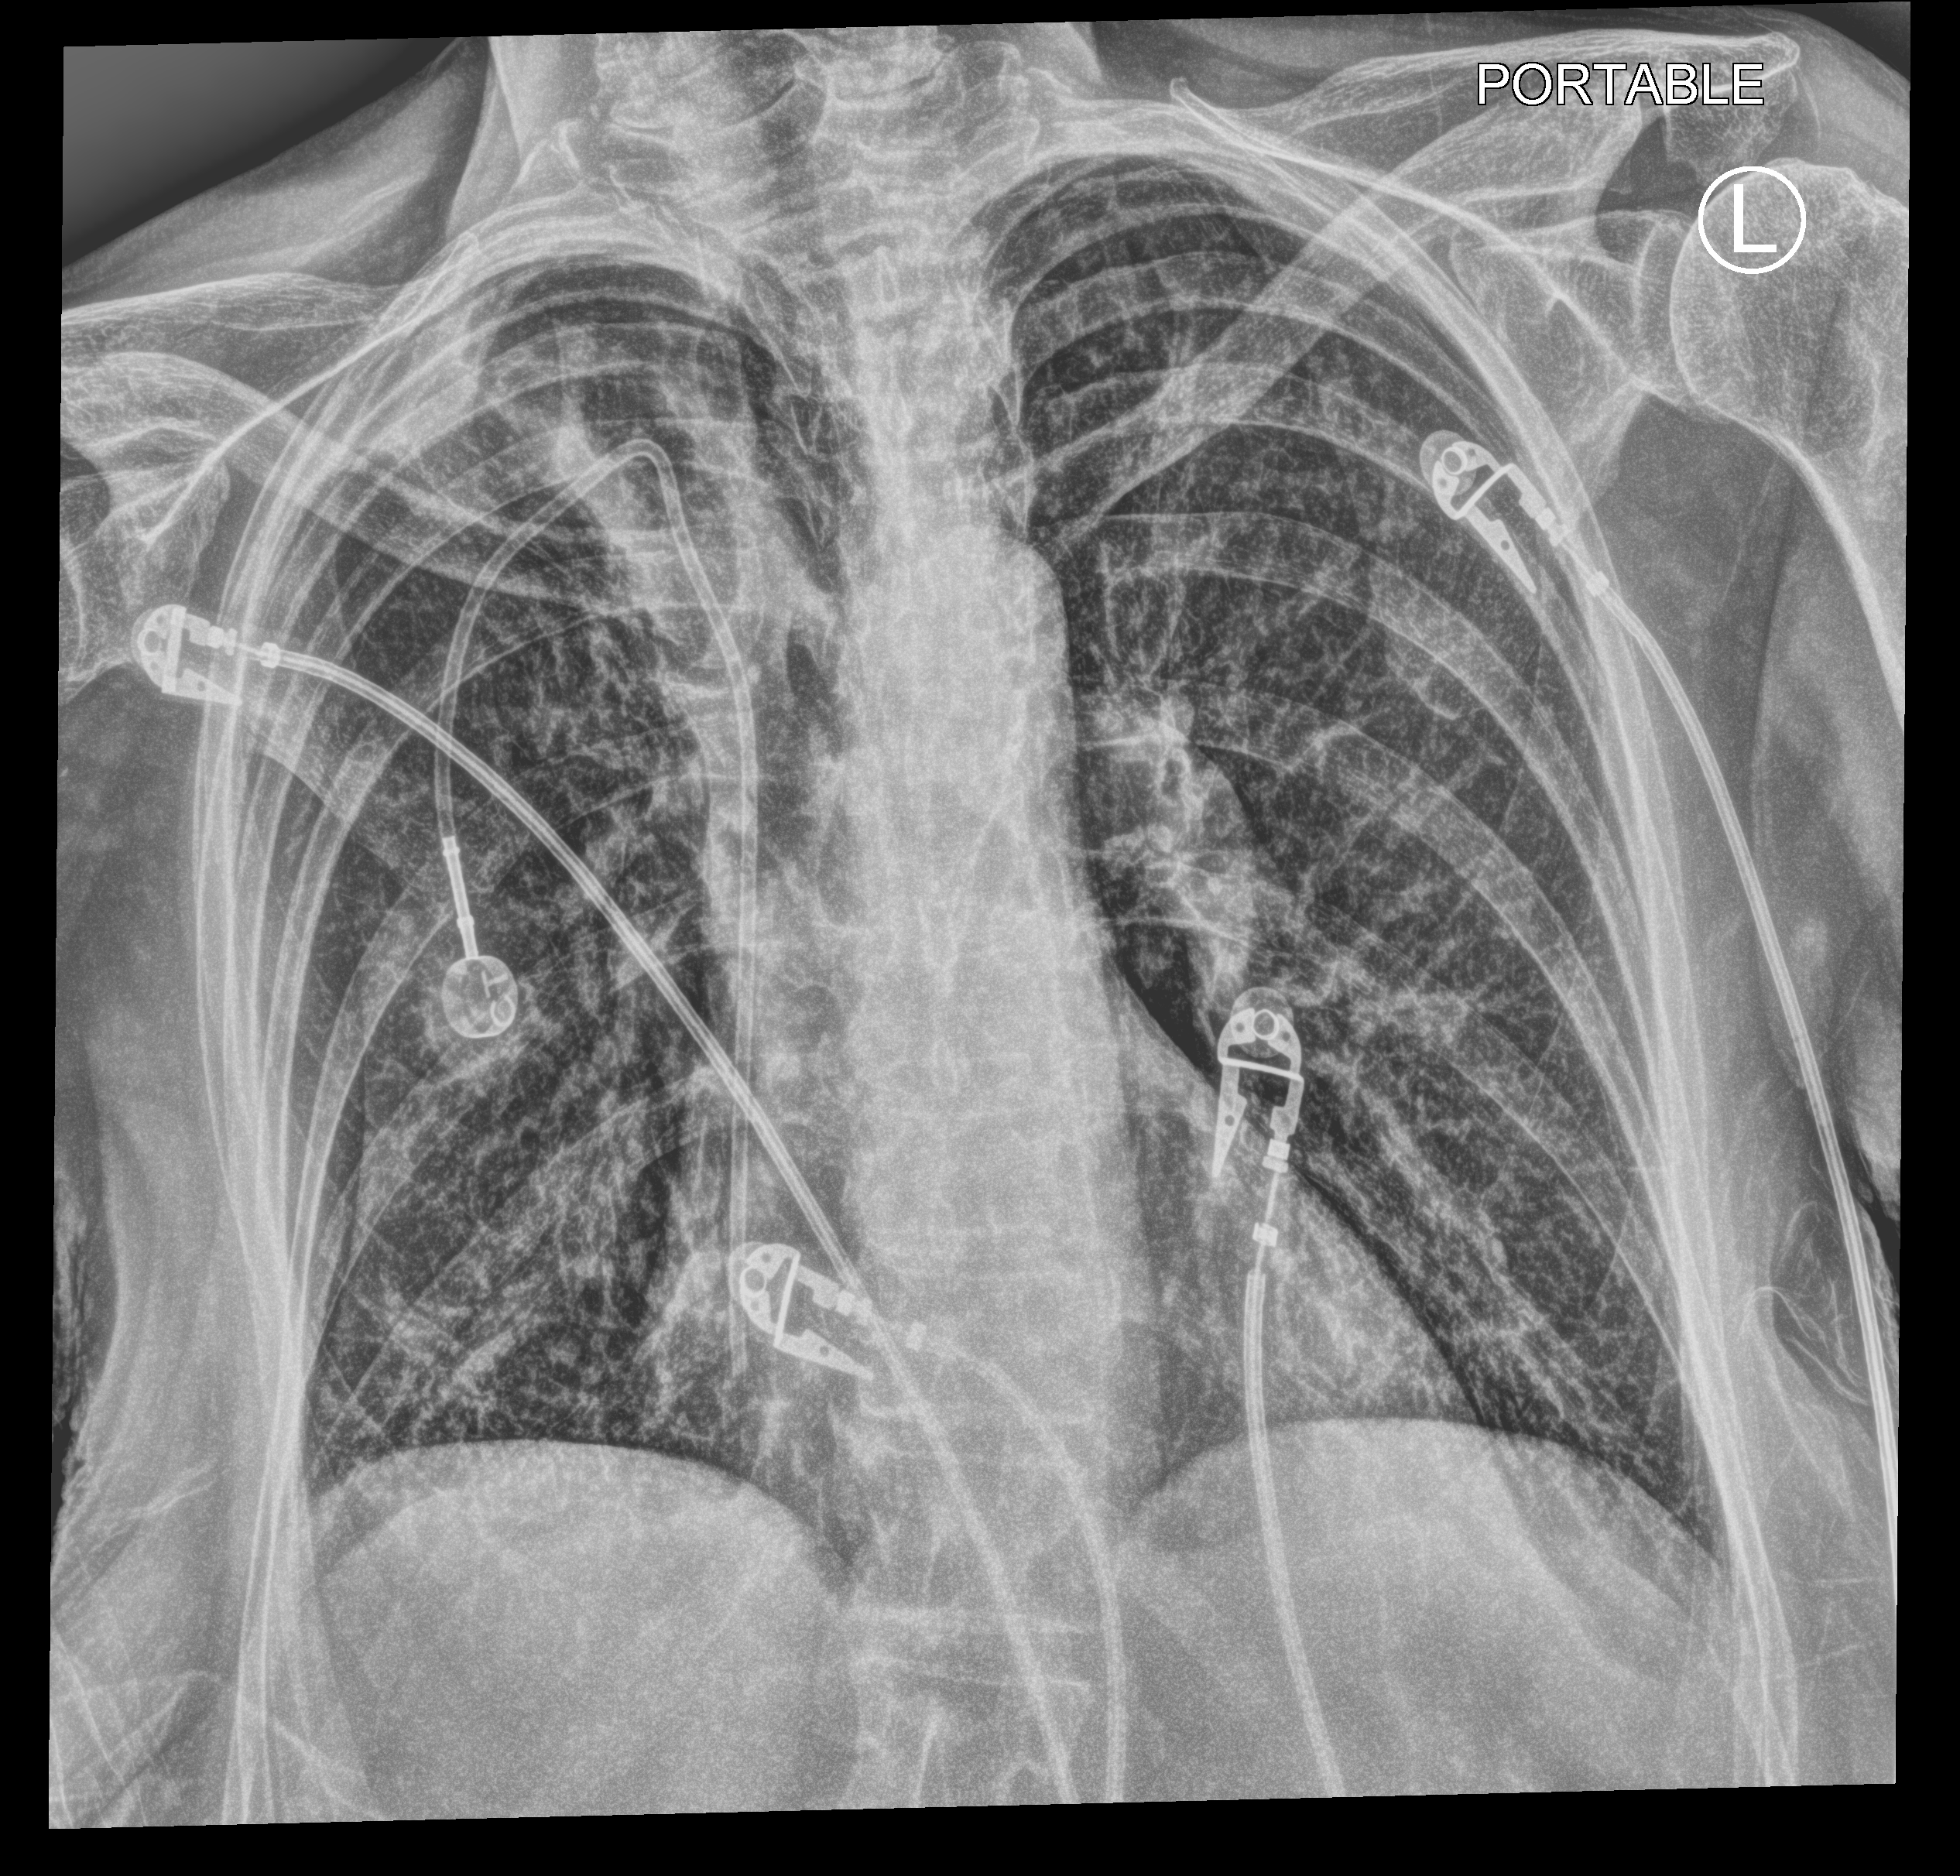
Chest X-ray (portable); anteroposterior (AP) projection. Patient hospitalised with COVID-19; female, aged 60–74 years.
From the hospital-stay record, not from the radiograph (when in the stay this image was taken is not recorded): length of hospital stay: 8 days; mechanically ventilated during this hospital stay: no; admitted to intensive care during this hospital stay: no.